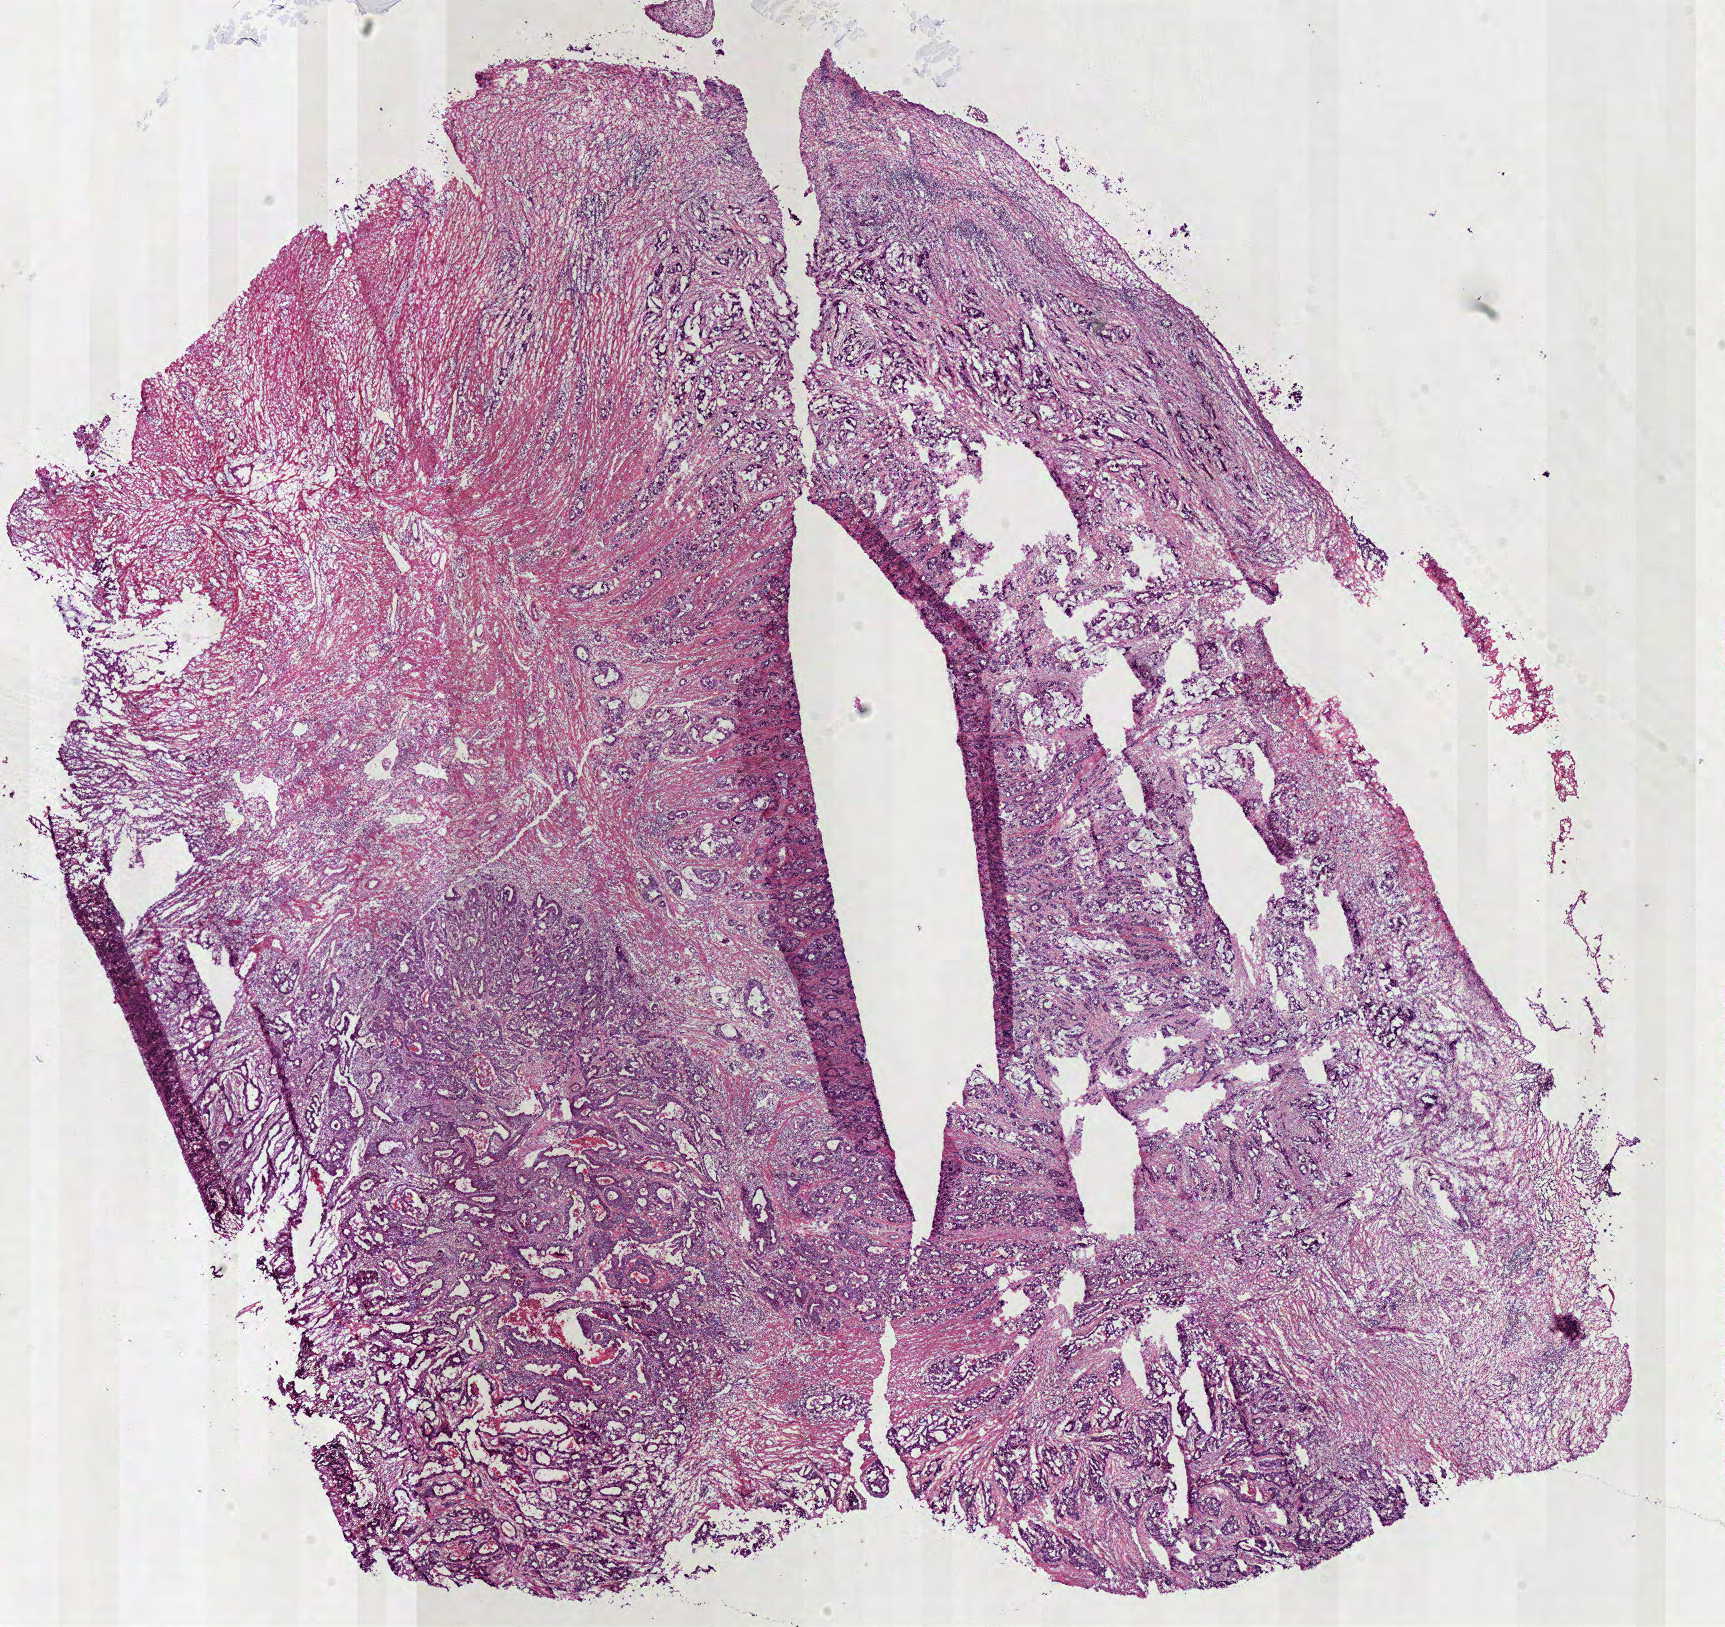
Whole-slide histology image, Hematoxylin and eosin (H&E) stained, a low-resolution overview of the entire scanned area, about 13.6 x 12.8 mm. Frozen section. Primary tumour sample from the rectum. Female patient; age at initial diagnosis 74 years. Slide review estimates, as recorded: tumour cells 65%, tumour nuclei 80%, normal cells 0%, stromal cells 30%, necrosis 5%.
AJCC pathologic stage: IIIB. Diagnosis: Adenocarcinoma, NOS. Lymph nodes positive (case pathology): 4 of 4 examined.